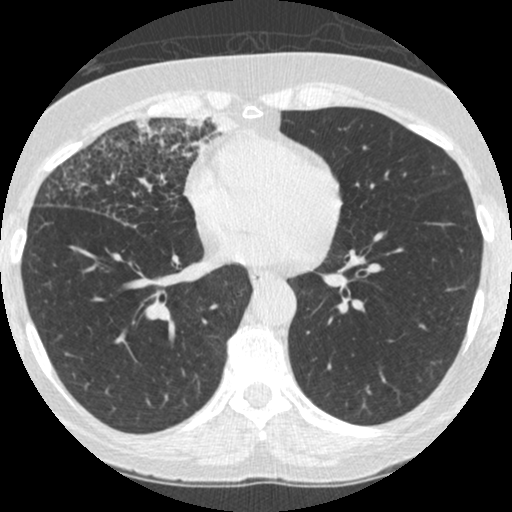
Low-dose screening chest CT, one axial slice. Slice 116 of 253 in the series (ordered by position). Lung window (W 1500 / L -600 HU). 1.25 mm slice thickness. 512 × 512 image matrix, field of view 294 × 294 mm.
Structures marked on this image (manually delineated by an expert):
- lesion 4 (tumor, upper lobe of right lung): bounding box <184,117,236,152> (left, top, right, bottom; pixels)